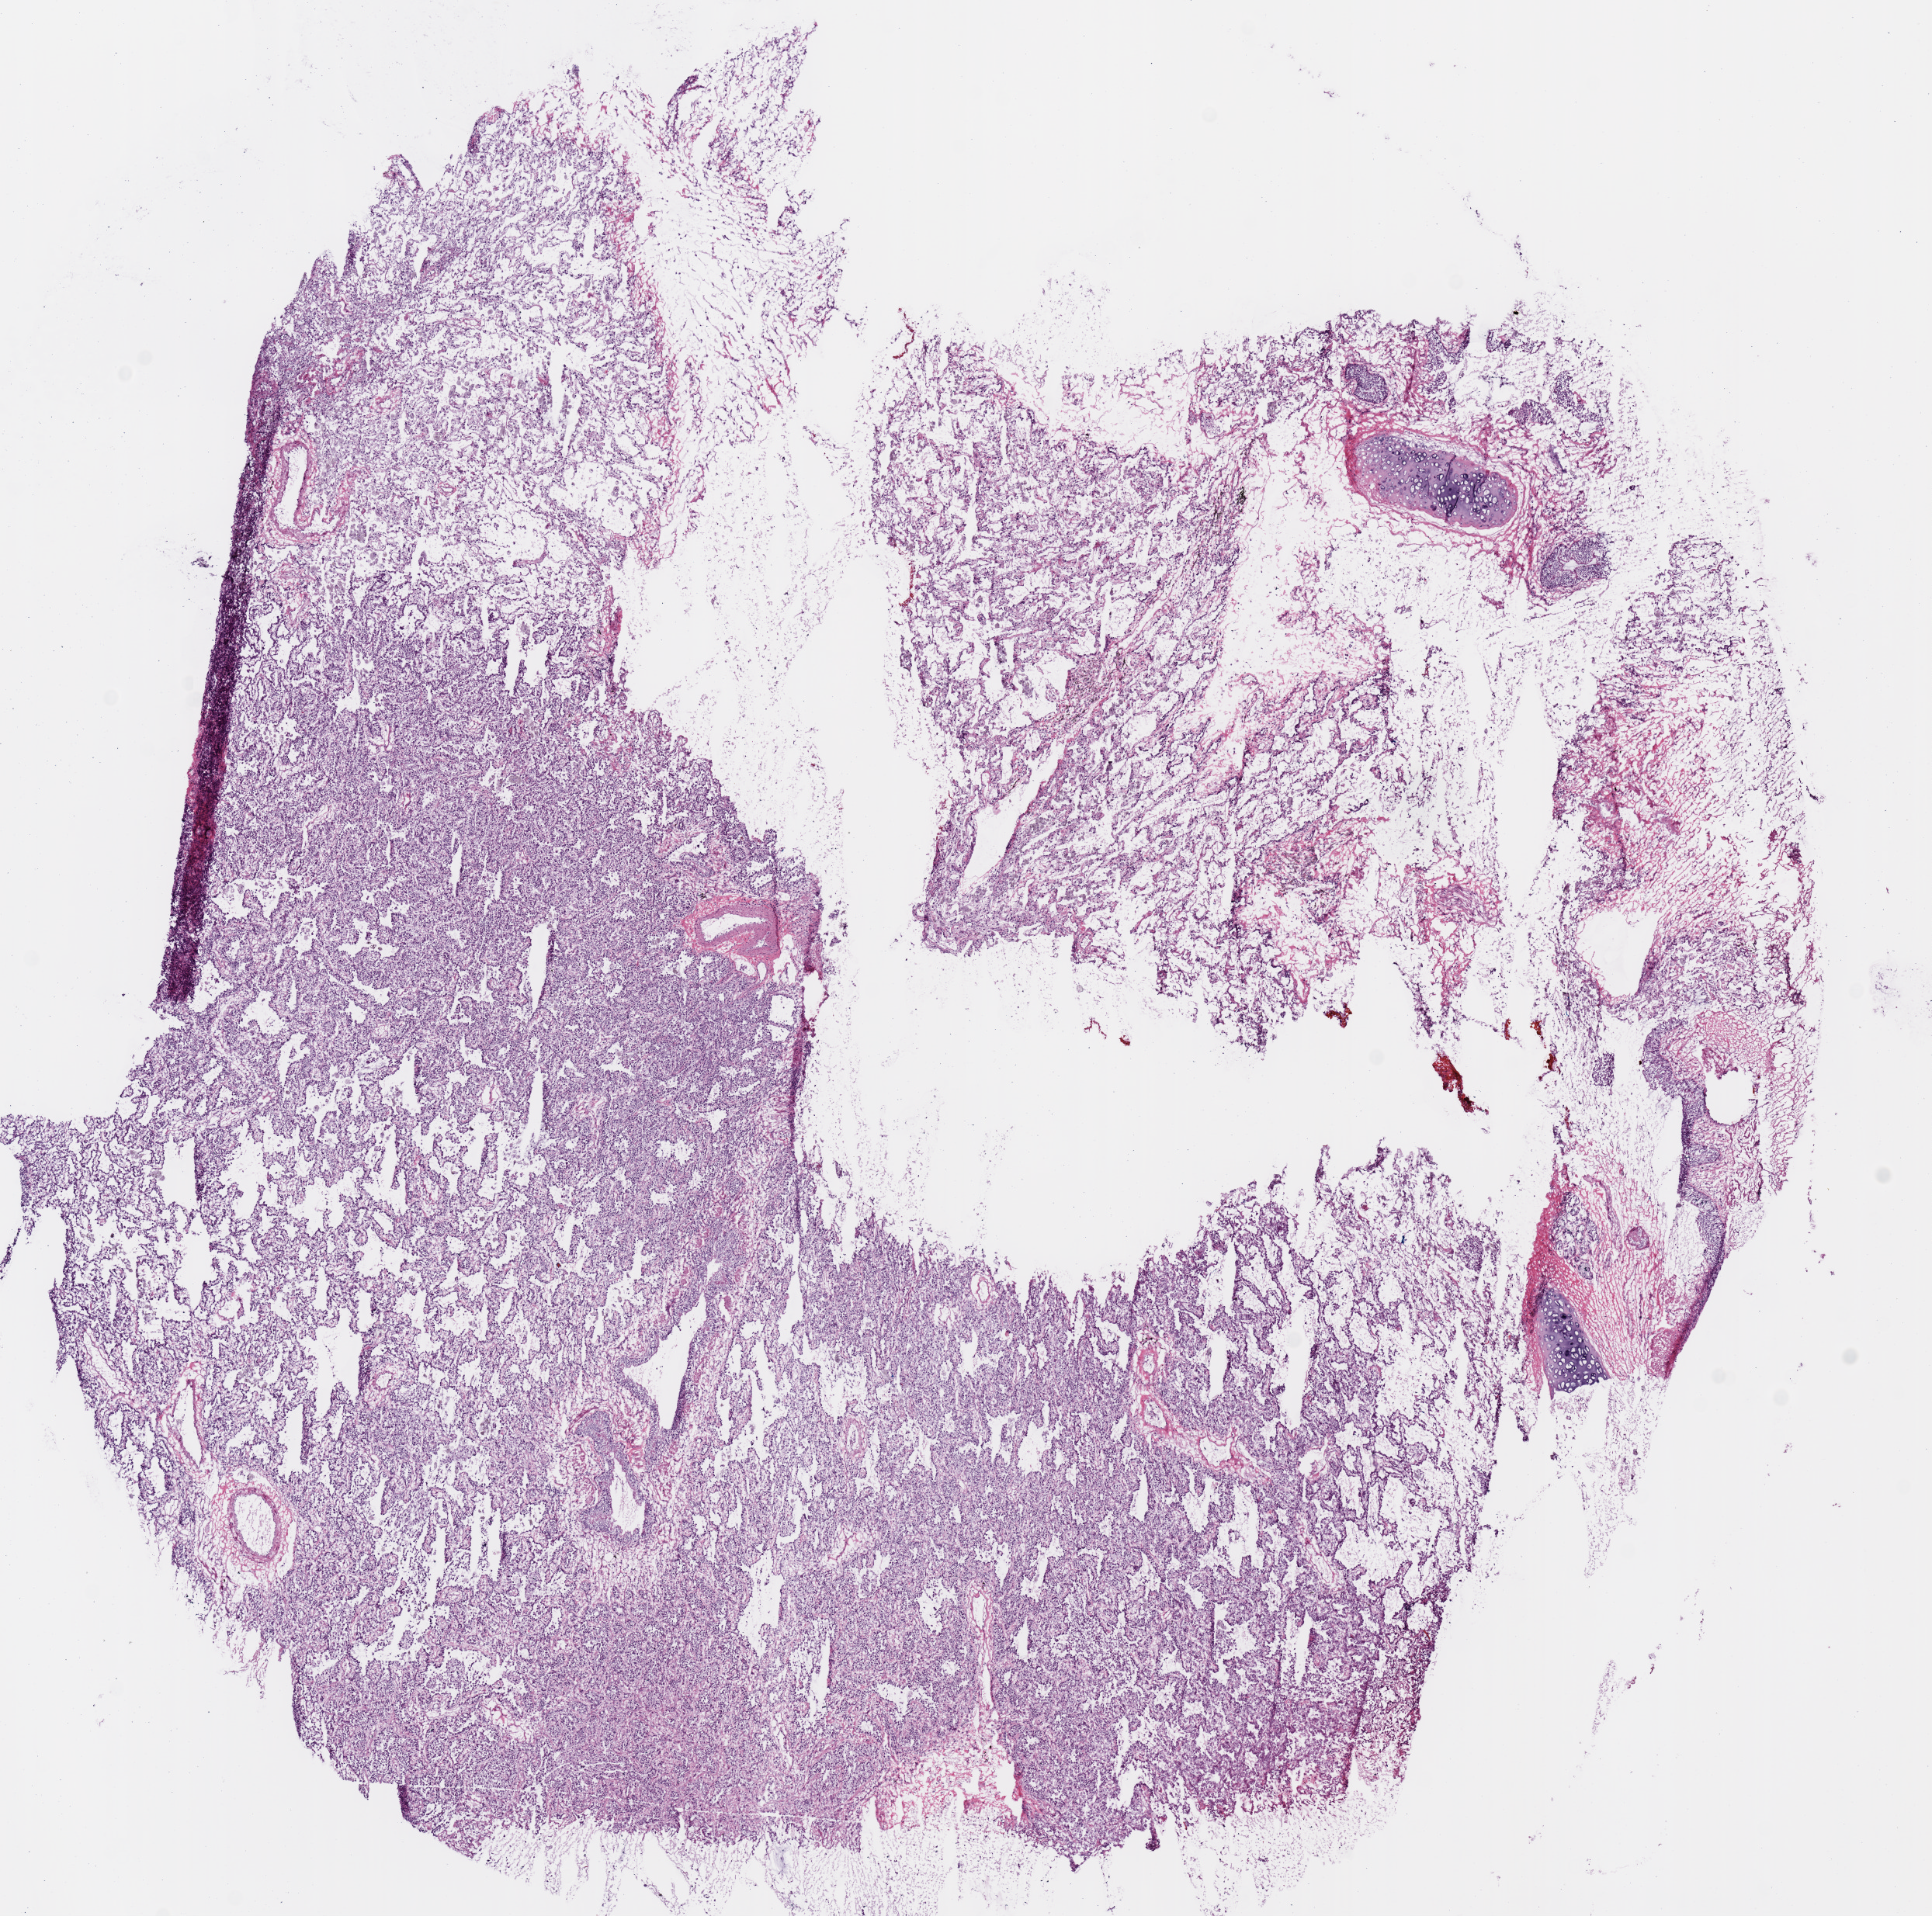
Digitized H&E tissue section (whole slide) — low-resolution overview of the scanned area, about 9.8 x 9.8 mm (from a 20x scan); frozen section from the top of the tissue portion; lung, primary tumour sample. Patient: male, age at initial diagnosis 41 years. Composition of this section per pathologist review: tumour nuclei 75%, necrosis 0%.
TNM: T1a N1 M1b. Laterality: right. AJCC pathologic stage: IV. Histologic diagnosis: Bronchiolo-alveolar carcinoma, non-mucinous (lower lobe, lung).